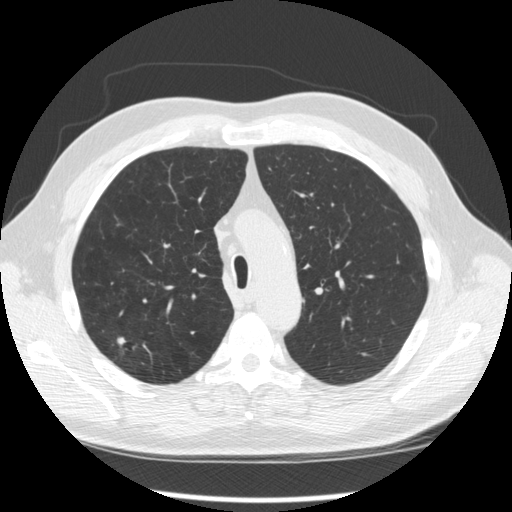
Axial slice from a low-dose chest CT screening exam. Second screening round (one year after baseline). Lung window (W 1500 / L -600 HU). 120 kVp. Slice 77 of 289 in the series. 512 × 512 image matrix. Male, age 64 years at enrolment. Former smoker at enrolment.
- Expert-annotated lung lesion, box from (x=107, y=324) to (x=150, y=365) px.
- The screening reader recorded 3 non-calcified nodules or masses ≥4 mm on this exam; which of them this box marks is not recorded.
- Lung cancer was diagnosed 411 days after this screen (after the third annual screen): adenocarcinoma, NOS, right upper lobe, moderately differentiated (G2), stage IA (AJCC 6th edition), 14 mm at pathology.